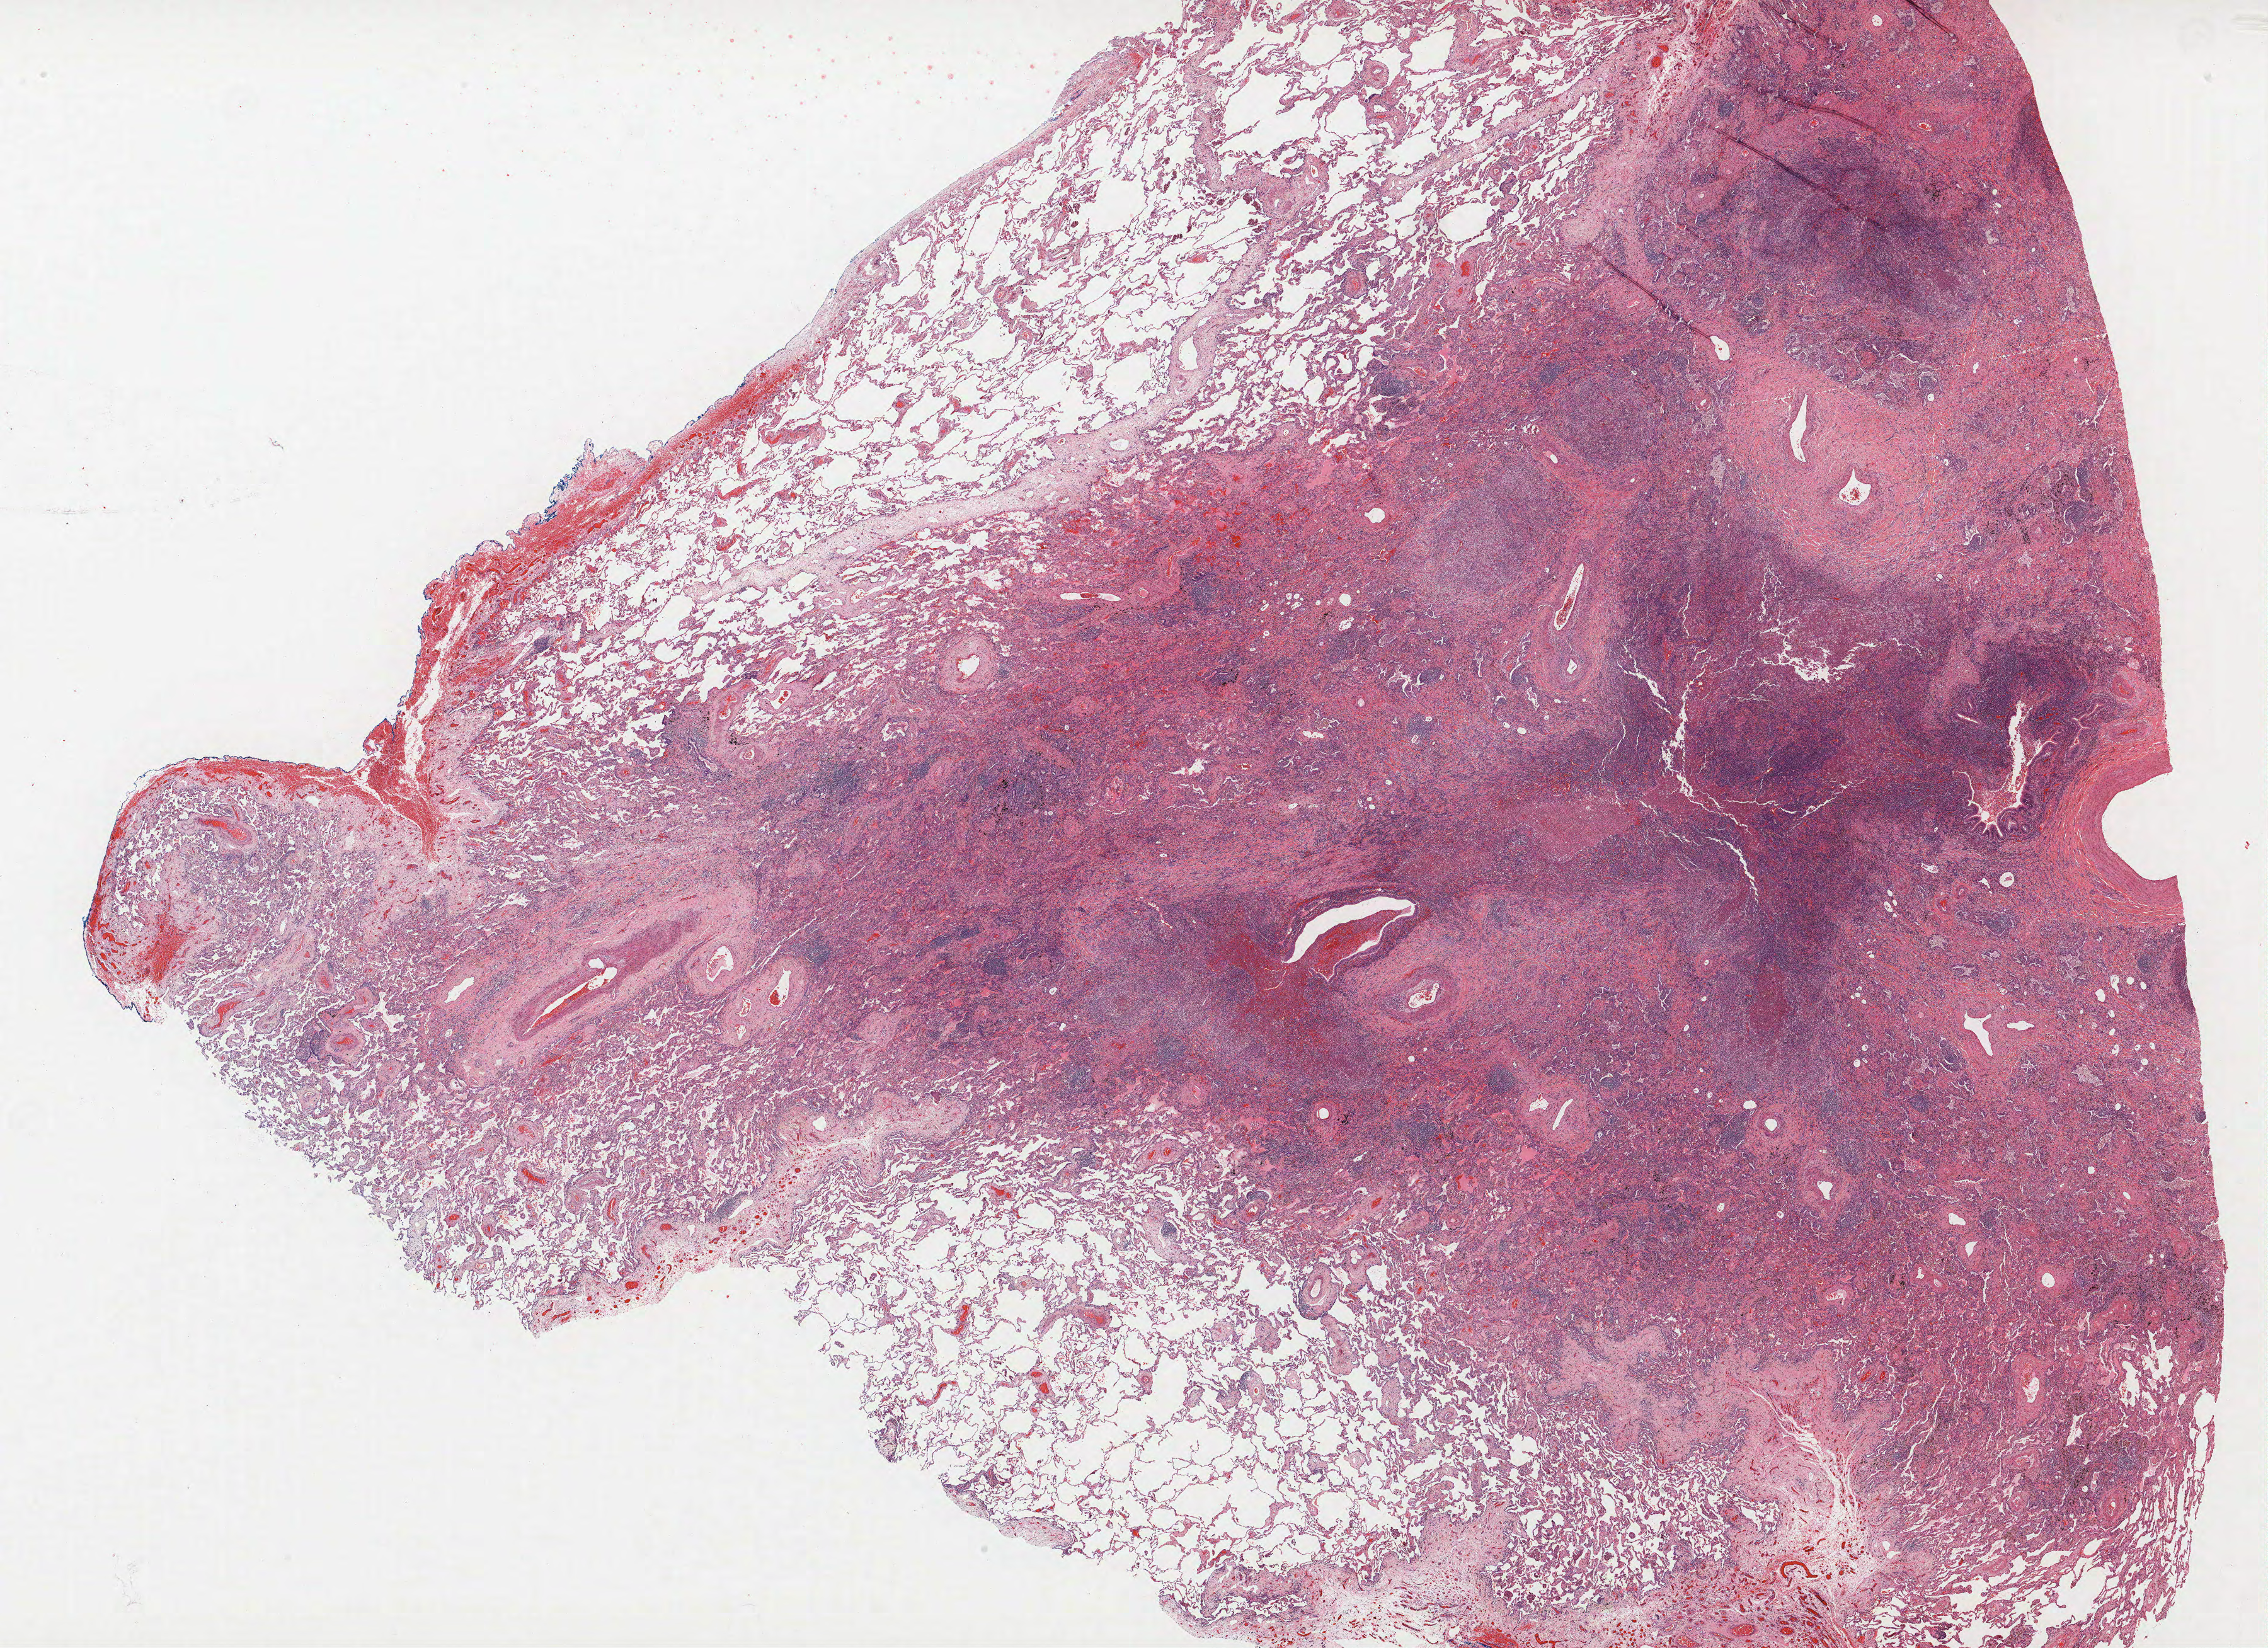
Whole-slide histology image, H&E, low-resolution overview of the scanned area, about 28.8 x 20.9 mm. Formalin-fixed paraffin-embedded (FFPE) section. Lung. Male, age 58 at enrolment. Current smoker at enrolment. Grade: moderately differentiated (G2).
ICD-O-3 topography: lower lobe of lung (C34.3). Tumour size (pathology): 11 mm. Participant's lung-cancer diagnosis: Squamous cell carcinoma, large cell, nonkeratinizing, NOS (ICD-O-3 8072/3). Stage (AJCC 6th edition): IA. Primary tumour location (clinical record): right lower lobe.